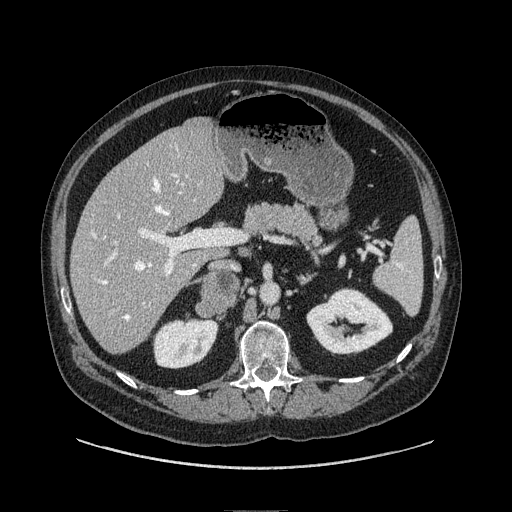
Contrast-enhanced abdominal CT, one axial slice. Slice 45 of 149 in the series (ordered by position). Soft-tissue window (W 400 / L 40 HU). 1.25 mm slice thickness. 512 × 512 image matrix, field of view 440 × 440 mm. Male patient. From the clinical record (not read from this slice): diagnosis: adrenocortical carcinoma; tumour side: right adrenal.
Structures marked on this image (semi-automatic segmentation, software-assisted and operator-edited):
- mass: bounding box <195,273,240,316> (left, top, right, bottom; pixels)